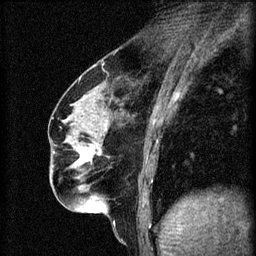
Breast MRI (dynamic contrast-enhanced), one sagittal slice. Slice 25 of 60 in the series (ordered by position). 3 images stored at this slice position (order not interpretable as contrast timing). 1.5 T. TE 4.2 ms, TR 8.2 ms. 2 mm slice thickness. 256 × 256 image matrix, field of view 180 × 180 mm. Patient: female, 56 years.
Annotated regions visible in this slice (semi-automatic segmentation, software-assisted and operator-edited):
- analysis volume of interest (the breast-tissue region the enhancement analysis was run in; not a lesion): bounding box (x1, y1, x2, y2) in pixels: (67, 136, 111, 179)
- tumour enhancement mask (voxels above the 70 % enhancement threshold inside the analysis volume of interest): (77, 144, 100, 163)